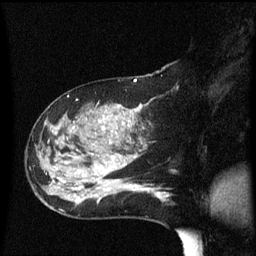
Breast MRI (dynamic contrast-enhanced), one sagittal slice. Position 26 of 60 along the scan axis. Dynamic contrast-enhanced series, image 2 of 3 at this slice position (ordered by acquisition). 1.5 T. TE 4.2 ms, TR 8.4 ms. 2.2 mm slice thickness. 256 × 256 image matrix. Patient: female, 47 years.
Structures marked on this image (semi-automatically segmented with operator editing):
- analysis volume of interest (the breast-tissue region the enhancement analysis was run in; not a lesion): box from (x=30, y=100) to (x=149, y=206) px
- tumour enhancement mask (voxels above the 70 % enhancement threshold inside the analysis volume of interest): (x=64, y=108)–(x=141, y=189)